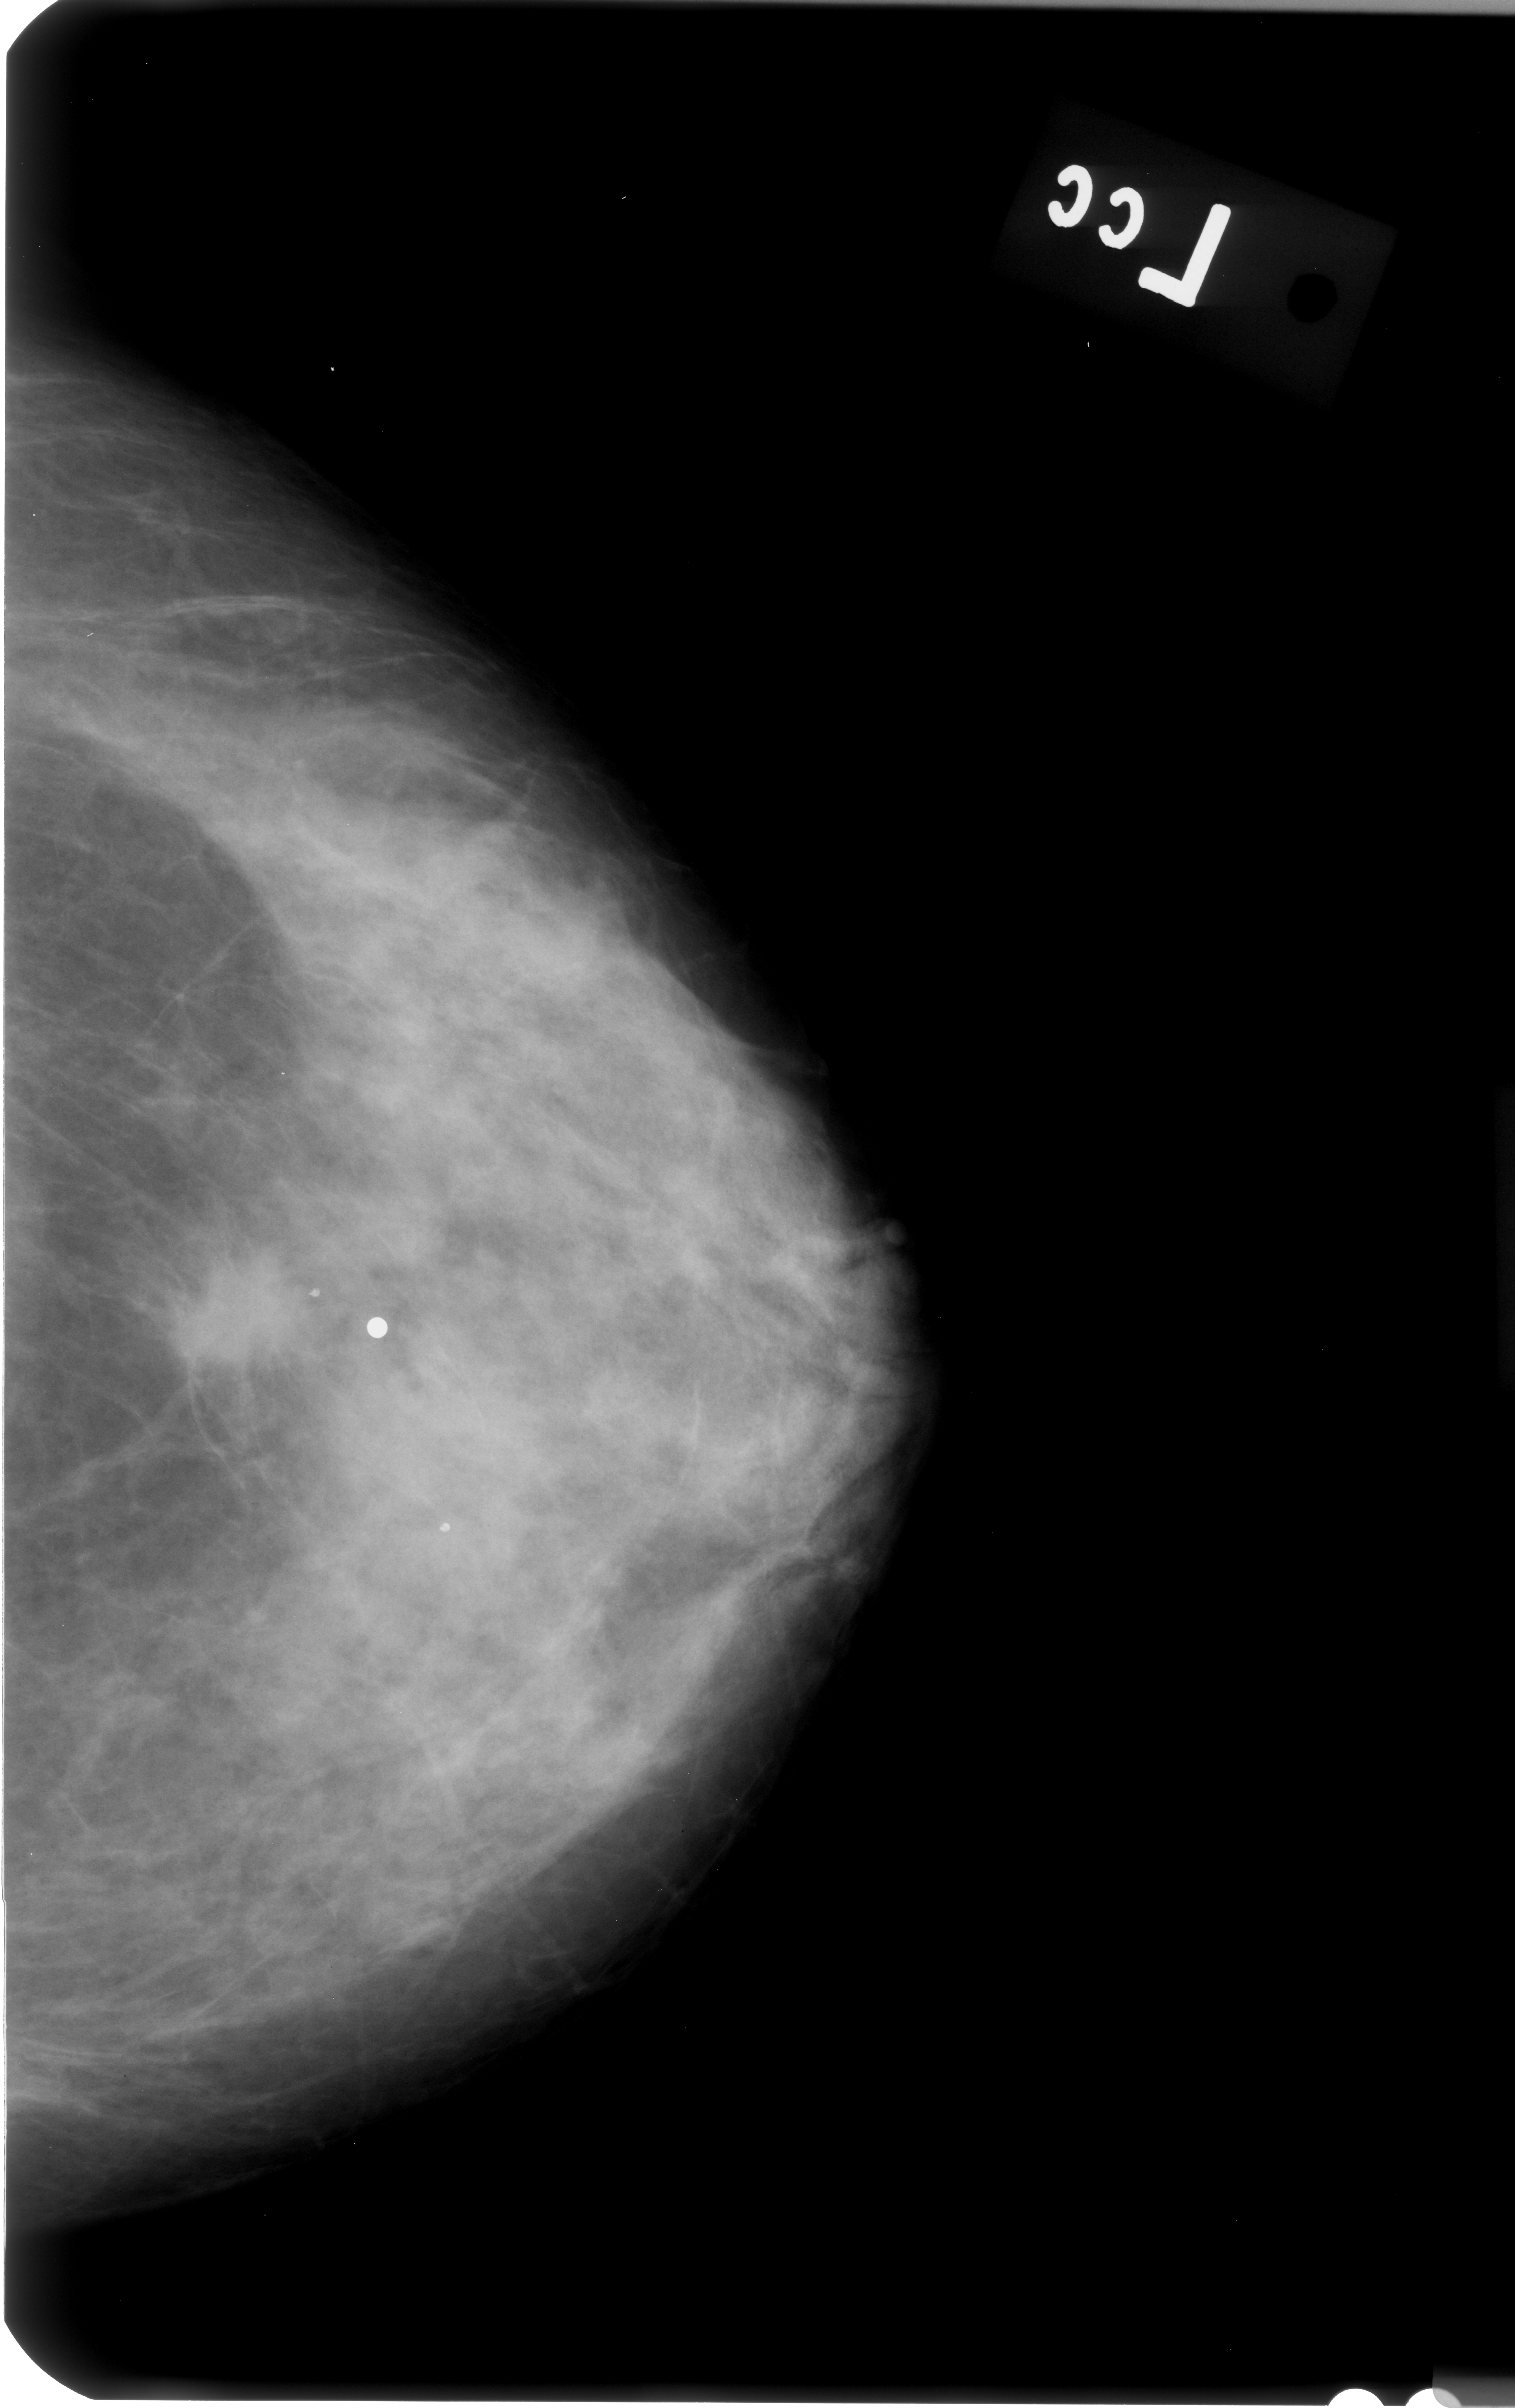
Digitized screen-film mammogram, left breast, CC view, breast composition: heterogeneously dense (BI-RADS density category 3 of 4).
Marked findings (only marked abnormalities are described; nothing is implied about the rest of the image): mass, shape irregular / architectural distortion, margins spiculated; BI-RADS assessment category 4; subtlety rating 4 on a 1 (subtle) to 5 (obvious) scale; pathology result (as recorded, not read from the image): malignant.